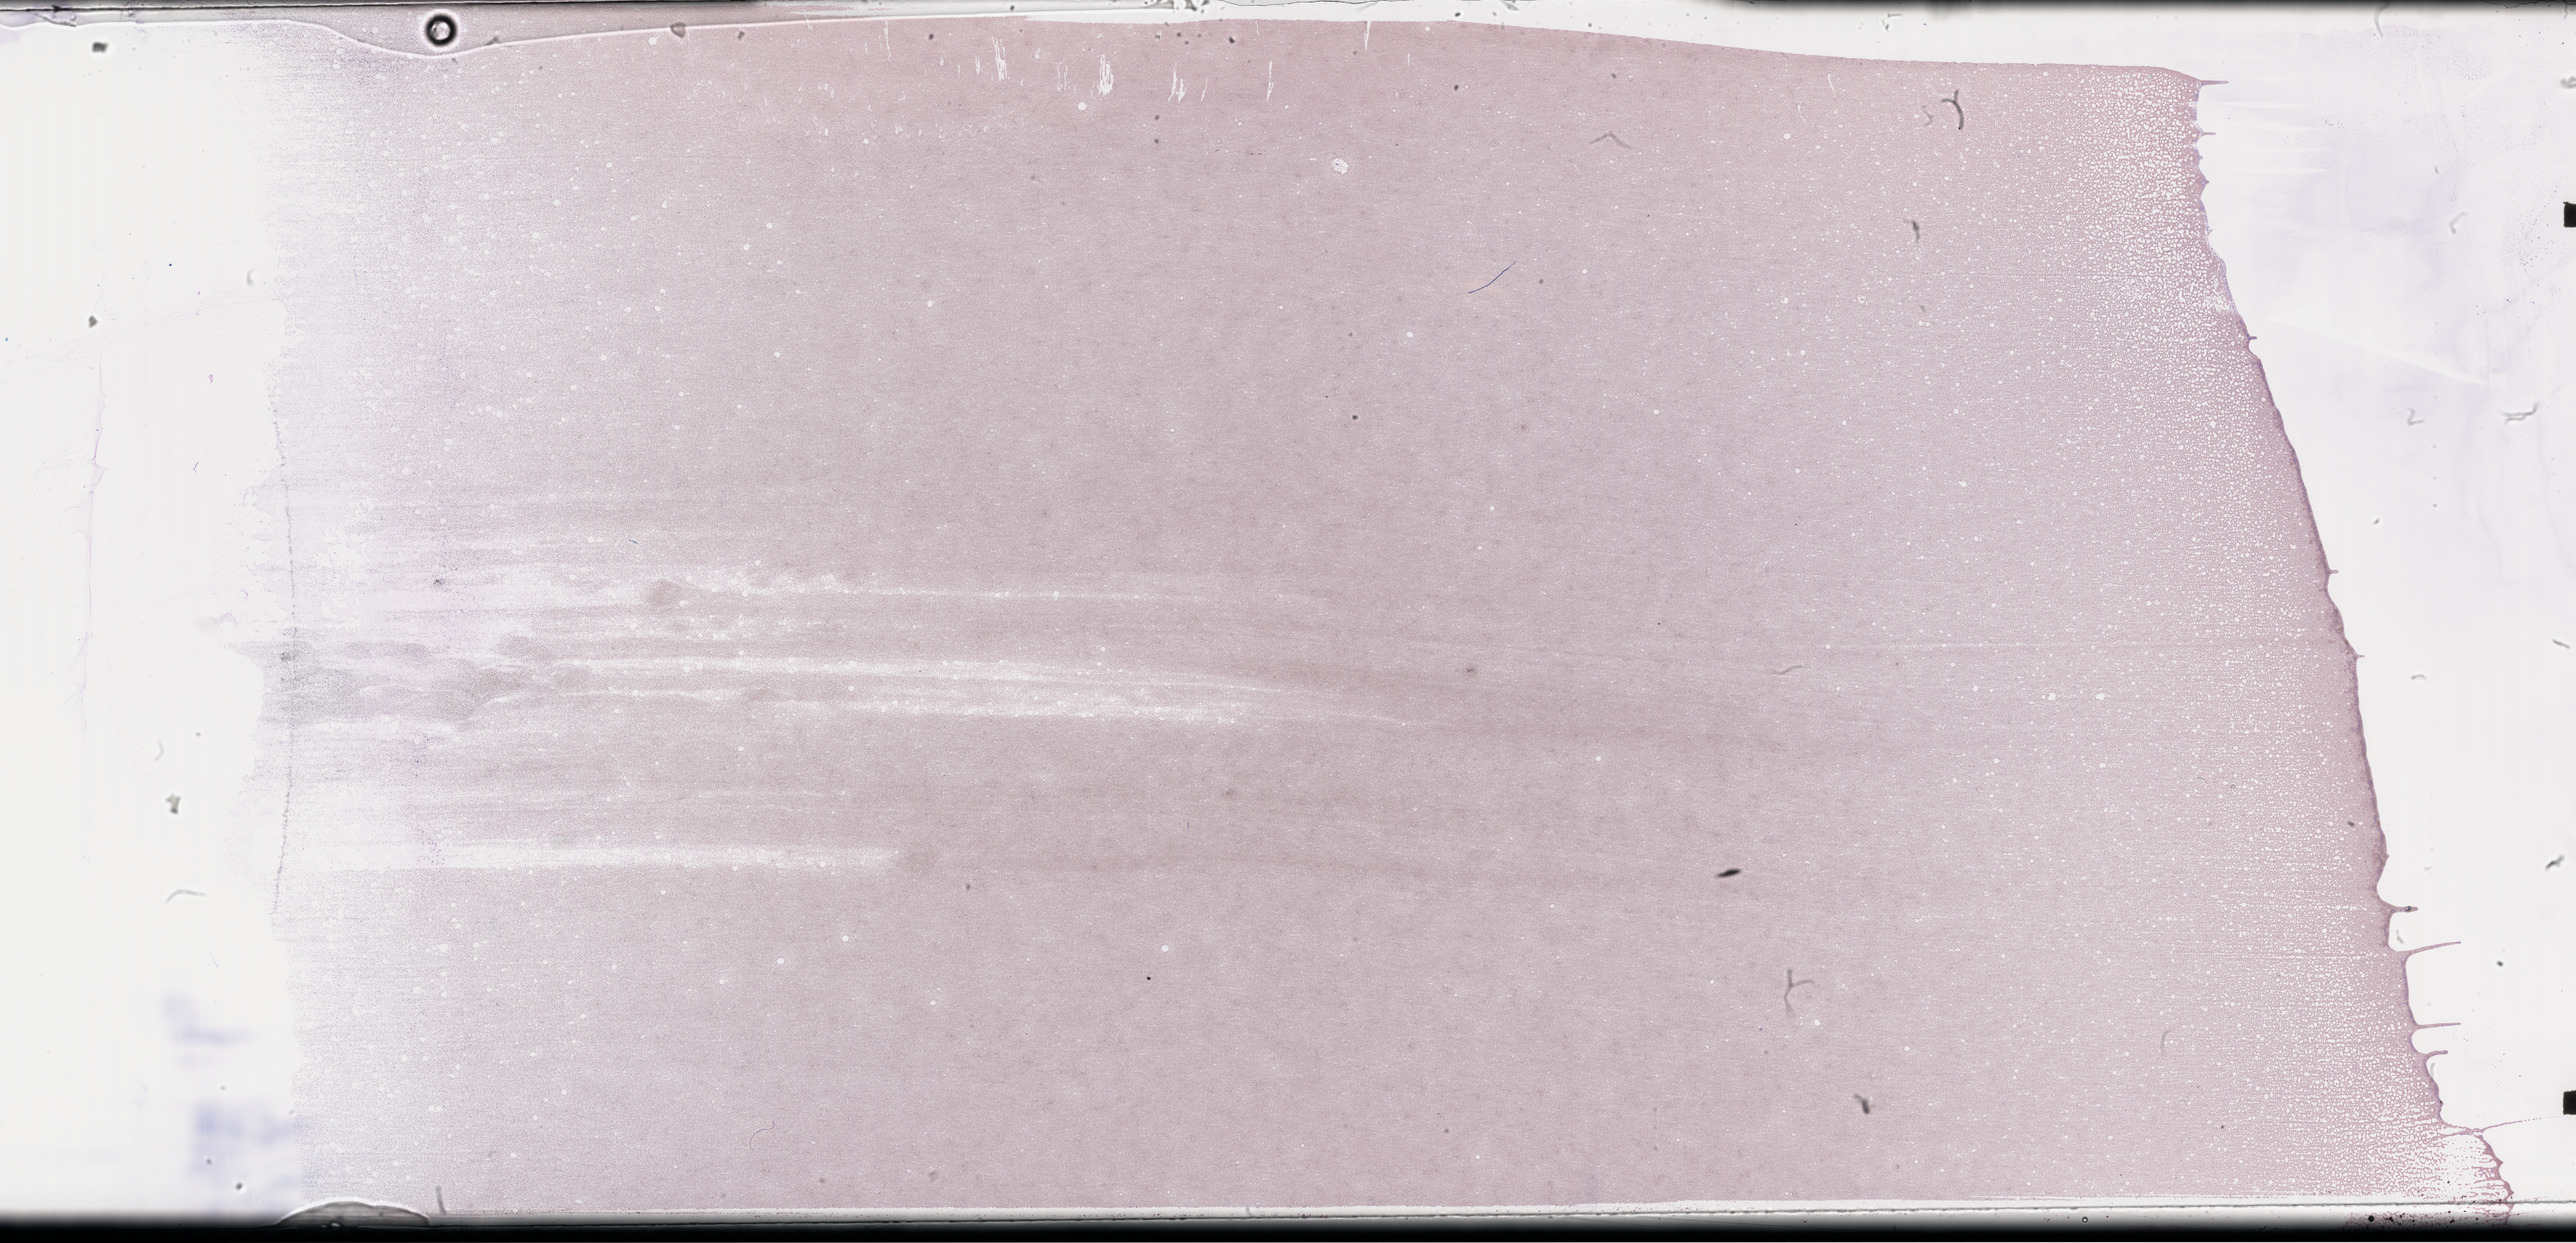
Wright–Giemsa-stained whole blood smear, whole-slide image, a low-resolution overview of the entire scanned area, about 50.8 x 24.5 mm, collected on treatment. Male patient.
Patient diagnosis: Plasma Cell Myeloma.